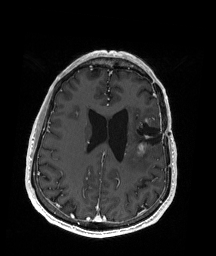
Brain MRI from a brain-tumour surgery series, one axial slice; position 71 of 192 along the scan axis; T1-weighted post-contrast; 1 mm slice thickness; 216 × 256 image matrix. Case-level facts recorded for this patient, not image findings: histopathology: Oligodendroglioma; WHO grade: 2; IDH mutation: yes; tumour location: Left Insular.
Structures marked on this image (expert manual segmentation):
- previous resection cavity: bounding box <132,121,163,148> (left, top, right, bottom; pixels)
- tumour: <137,117,153,155>